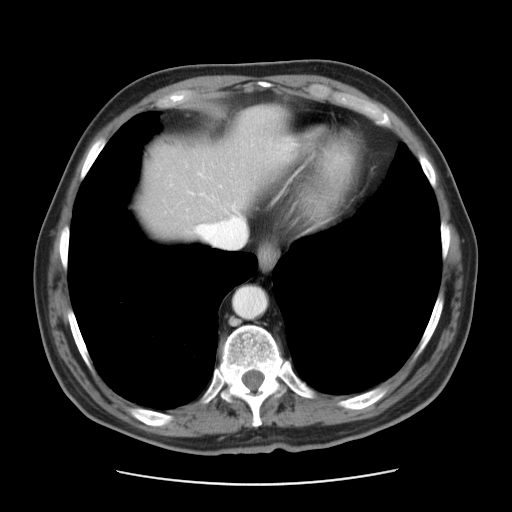
Contrast-enhanced abdominal CT, one axial slice; slice 38 of 42 in the series (ordered by position); reconstruction kernel STANDARD; intravenous contrast given; soft-tissue window (W 400 / L 40 HU); 512 × 512 image matrix, field of view 370 × 370 mm. Male patient, age 73 years. From the clinical record (not read from this slice): diagnosis: colorectal cancer liver metastases, imaged before liver resection; multiple liver metastases: yes; largest metastasis: 0.5 cm; disease in both lobes: no.
Outlined on this slice (outlined manually by an expert reader):
- hepatic veins: bounding box [x1, y1, x2, y2] px = [186, 165, 246, 249]
- liver: [145, 110, 289, 238]
- planned liver remnant (the part of the liver to remain after resection): [154, 110, 290, 221]